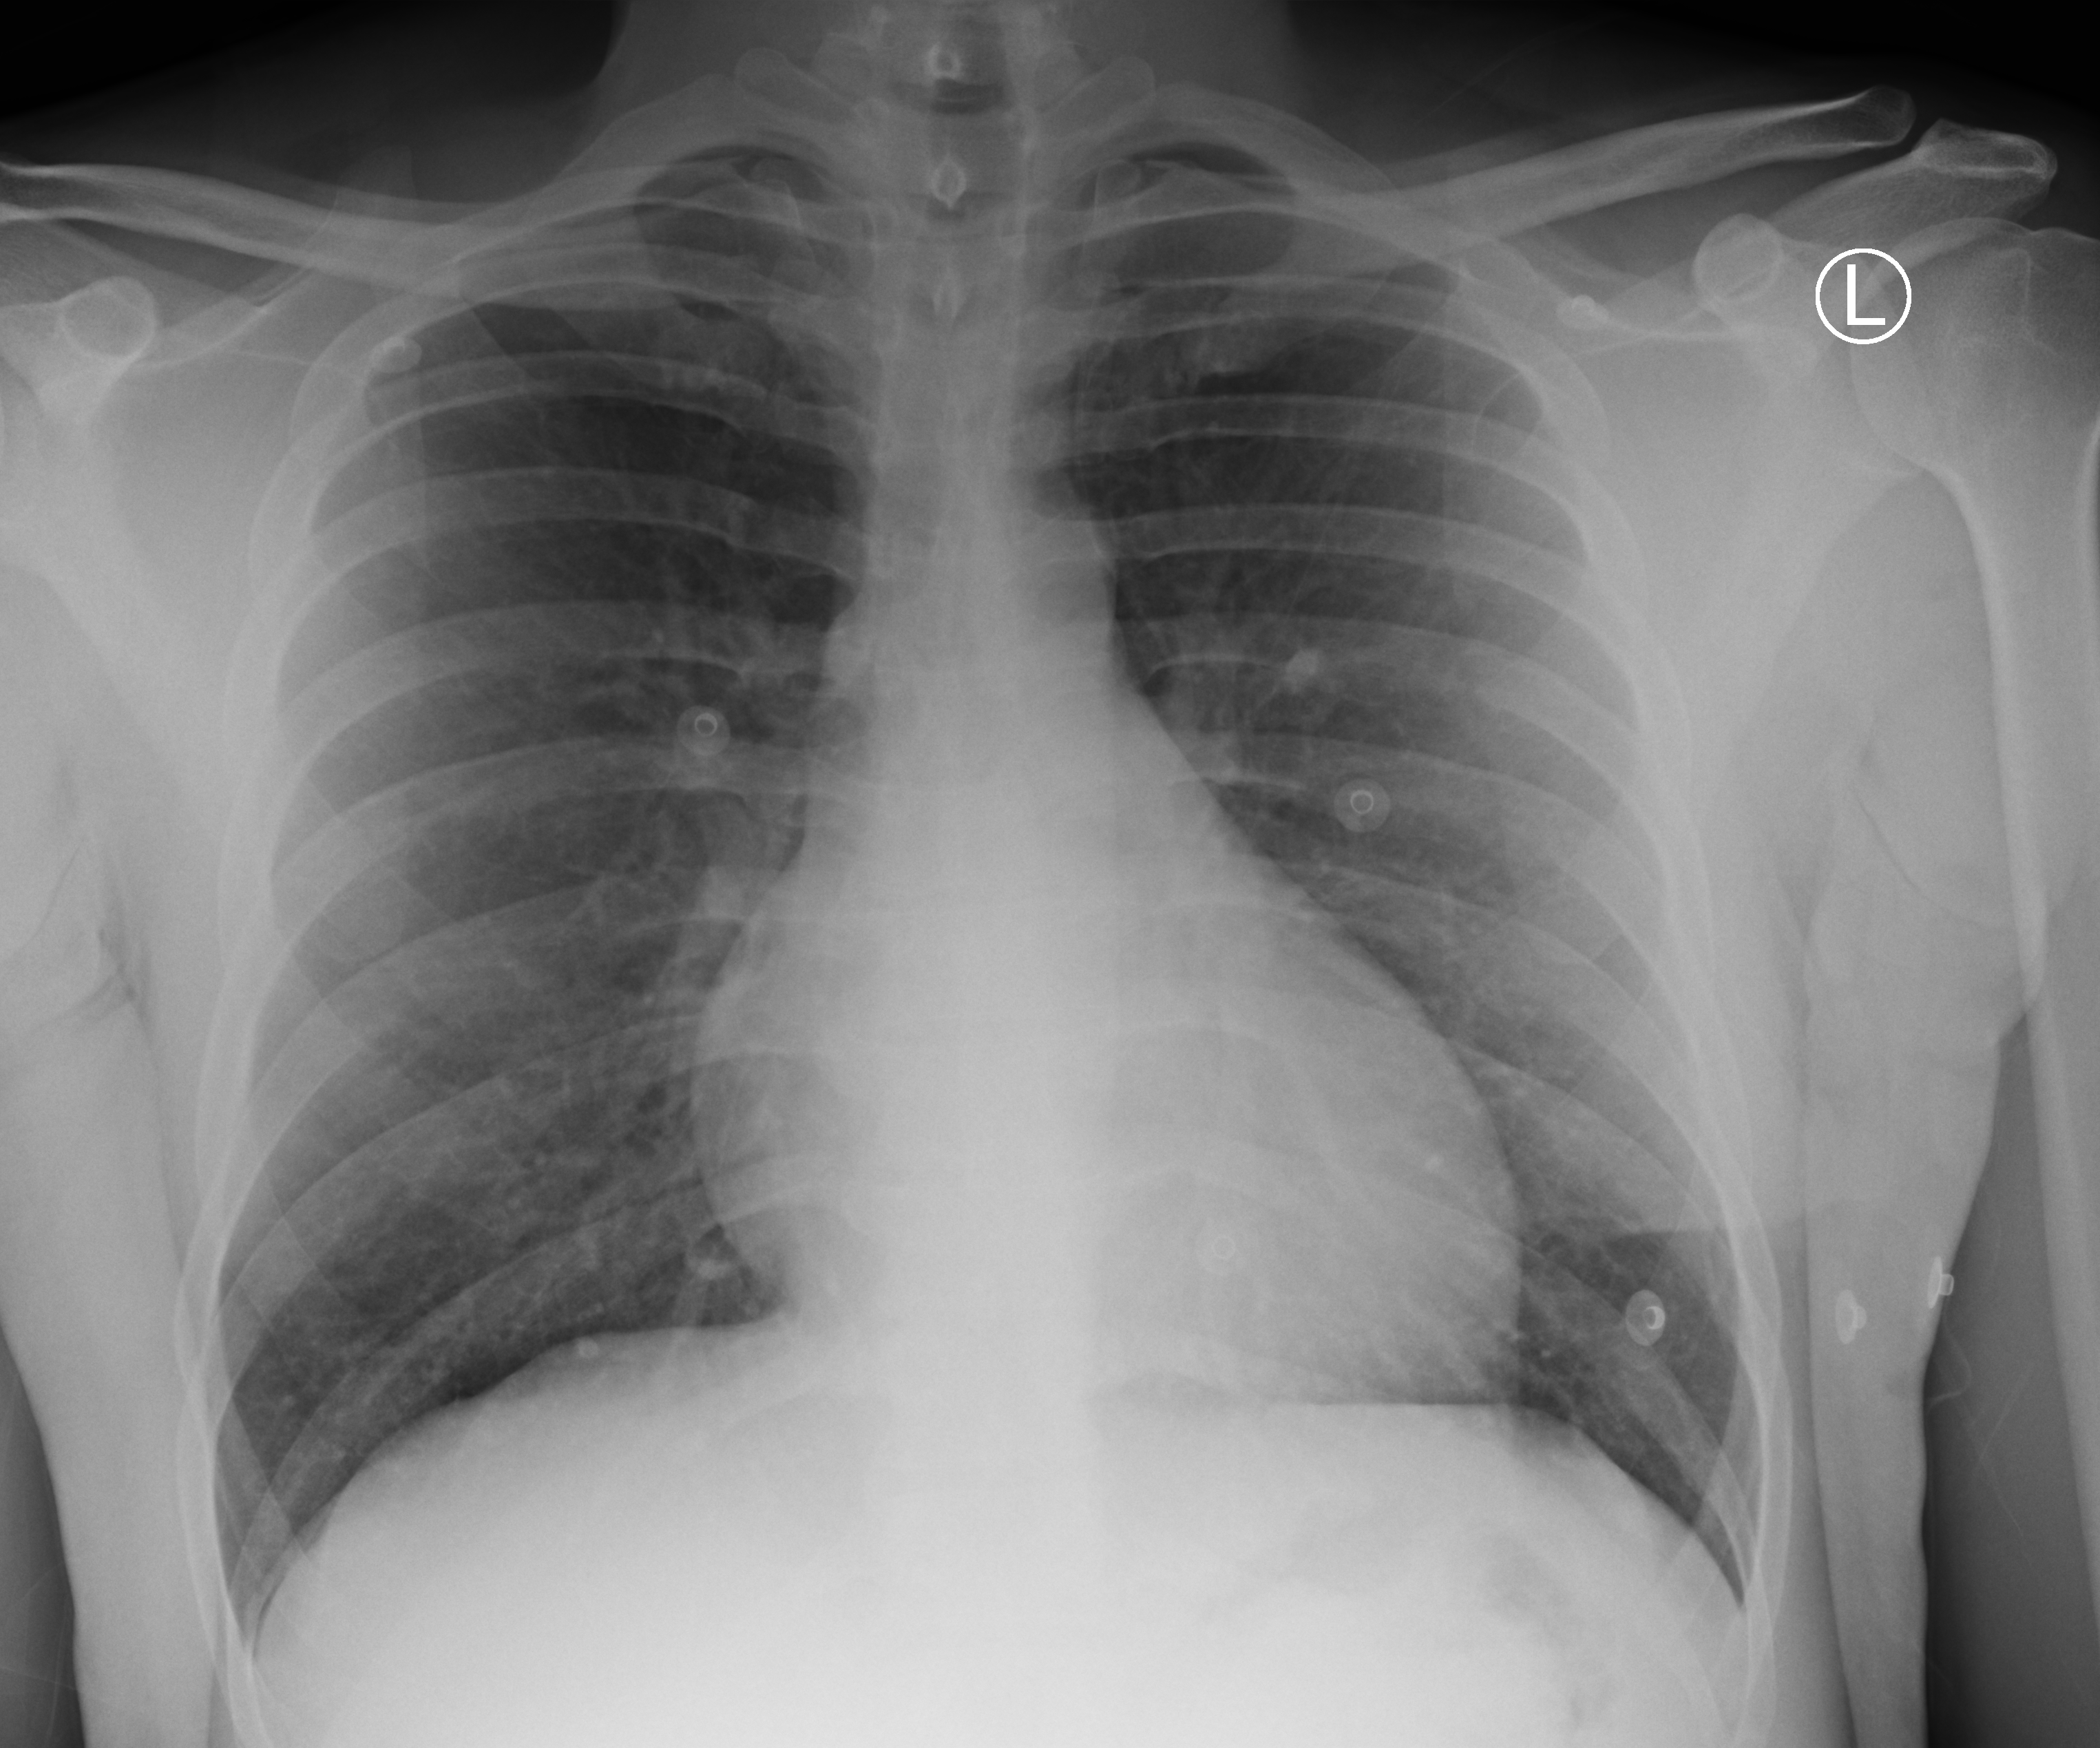
Bedside chest radiograph (computed radiography). Male patient hospitalised with COVID-19, age 18–59 years.
From the hospital-stay record, not from the radiograph (when in the stay this image was taken is not recorded):
- admitted to intensive care during this hospital stay: no
- mechanically ventilated during this hospital stay: no